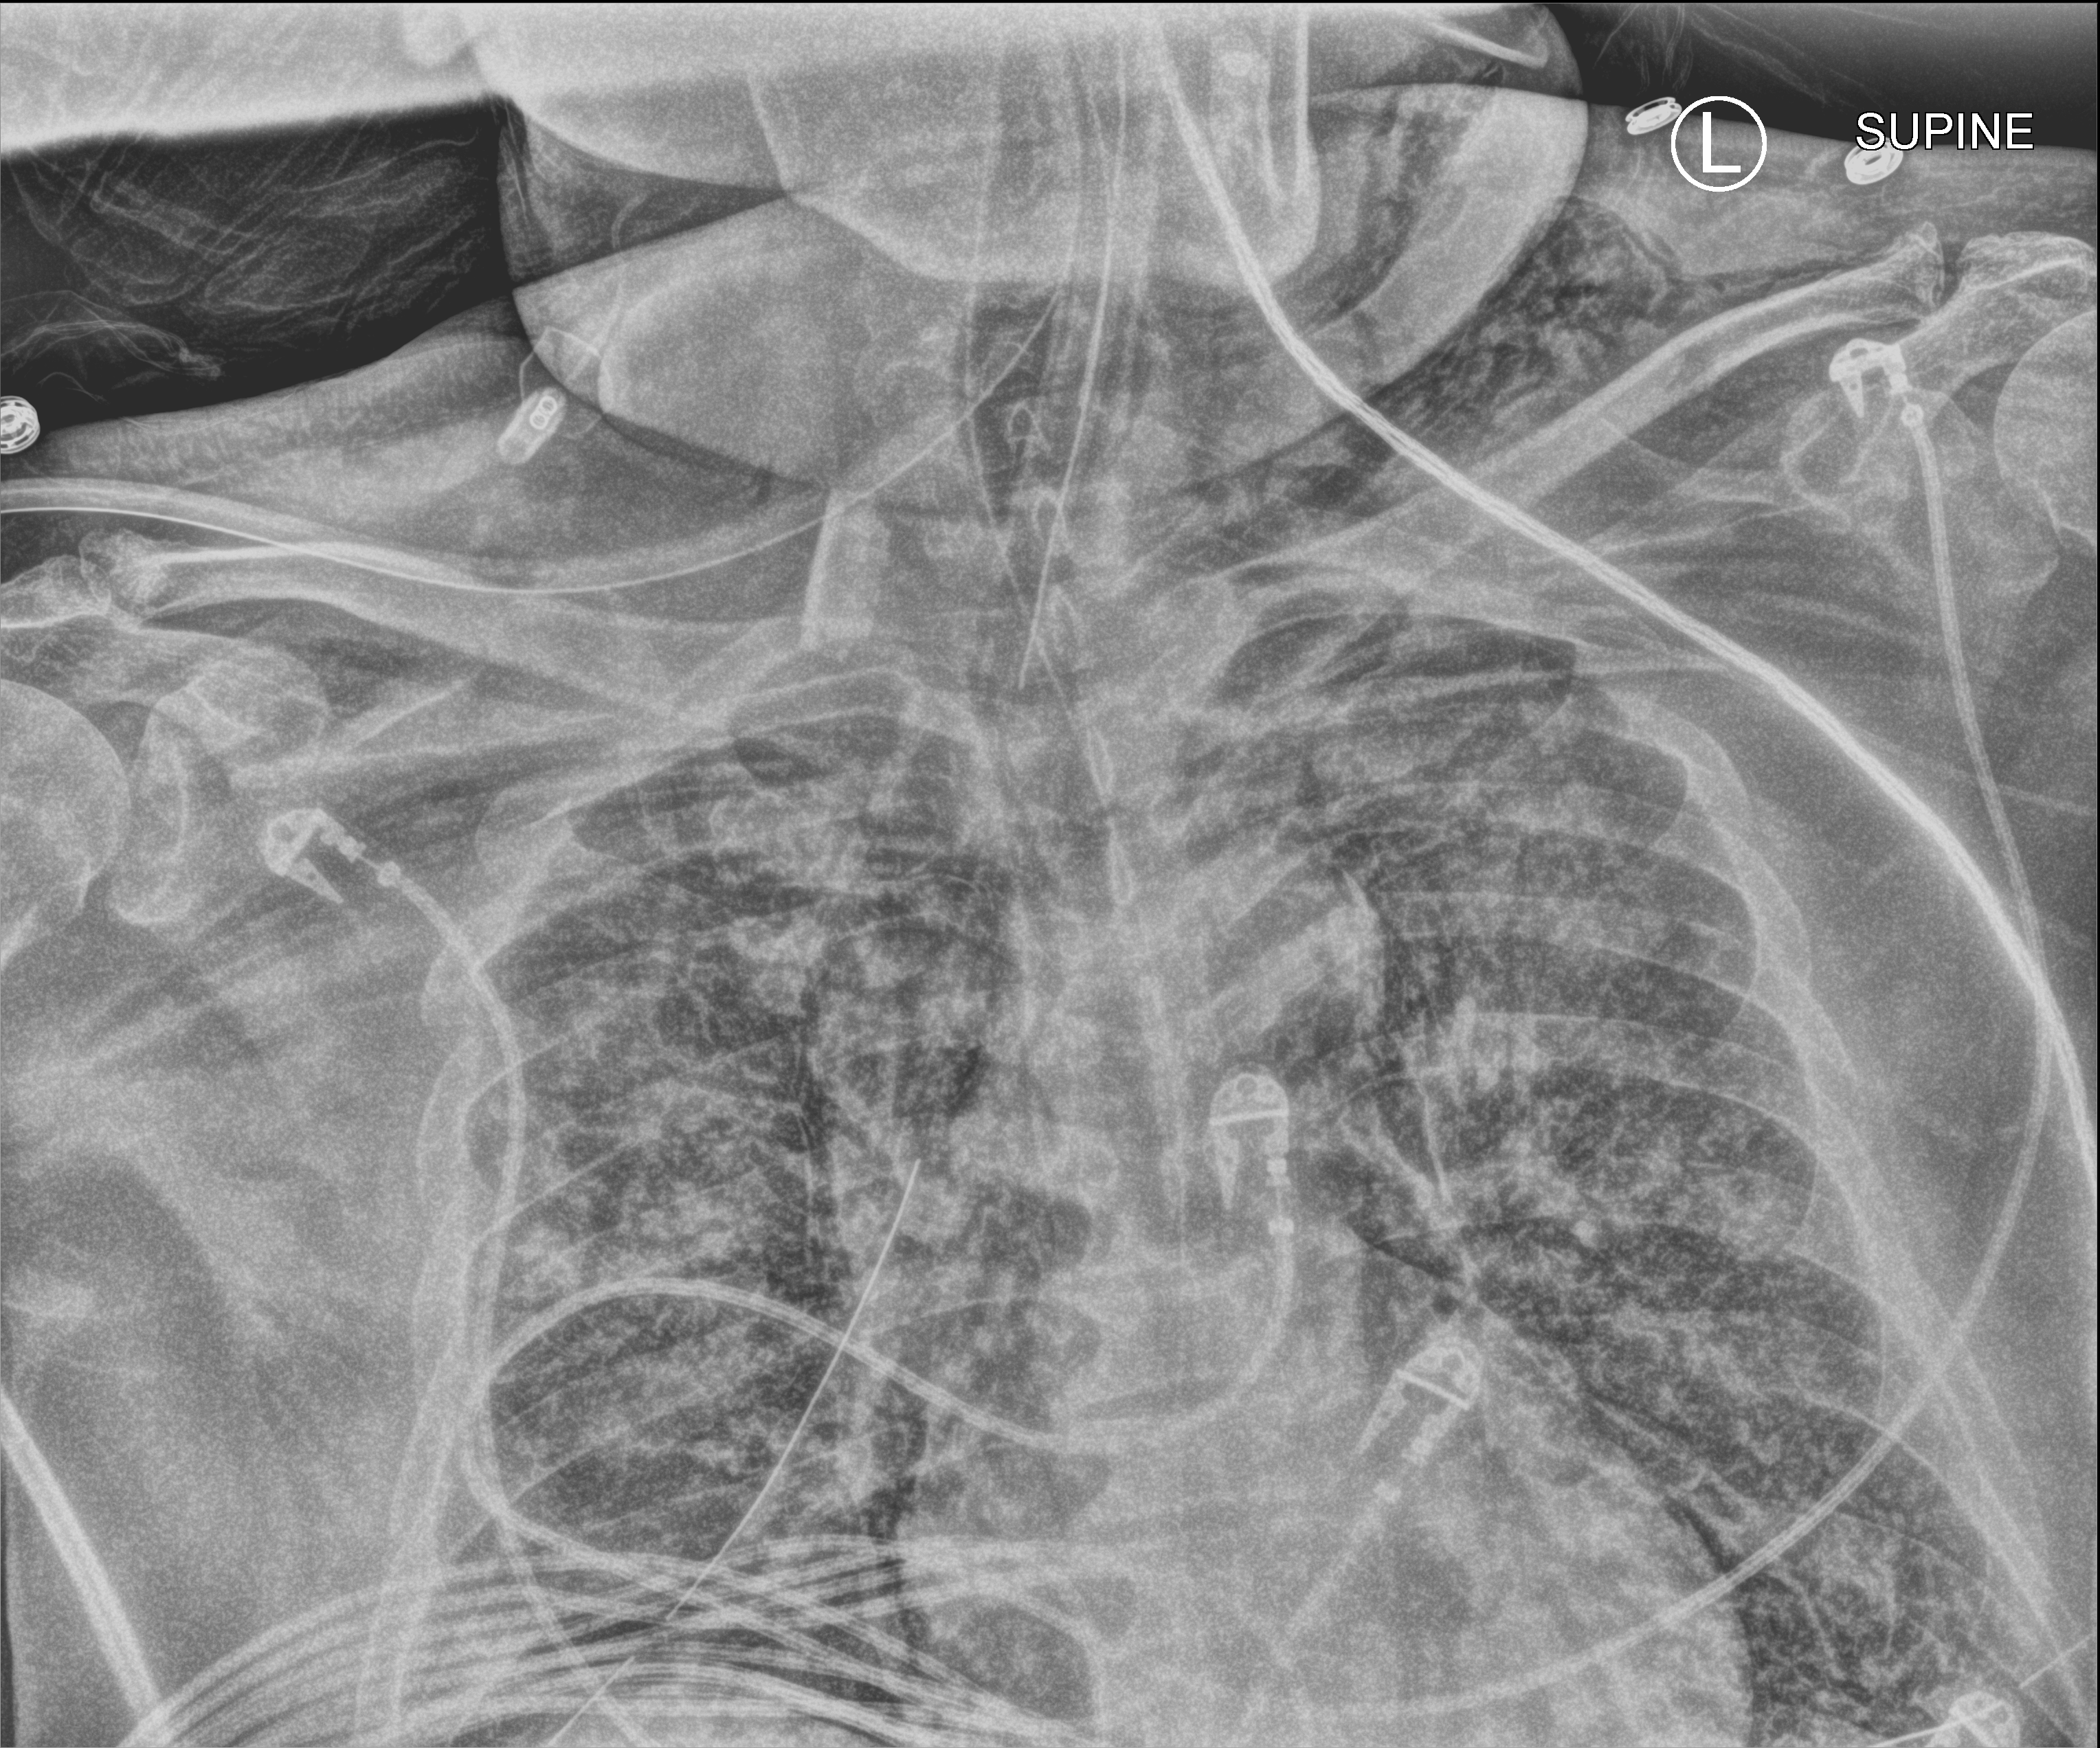
Bedside chest radiograph (computed radiography); anteroposterior (AP) projection. Patient hospitalised with COVID-19, aged 18–59 years.
From the hospital-stay record, not from the radiograph (when in the stay this image was taken is not recorded):
- mechanically ventilated during this hospital stay: yes
- length of hospital stay: 28 days